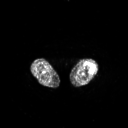
FDG PET of an extremity soft-tissue mass (from a PET/CT study), one axial slice; slice 192 of 267 in the series (ordered by position); 128 × 128 image matrix. Female patient, age 62 years. Case-level facts recorded for this patient, not image findings: histological type: undifferentiated – high grade; grade: high; site of the primary tumour: left thigh.
Structures marked on this image (expert contour drawn on MRI and transferred to this co-registered scan by the dataset authors):
- gross tumour volume including surrounding oedema: box from (x=86, y=63) to (x=94, y=72) px